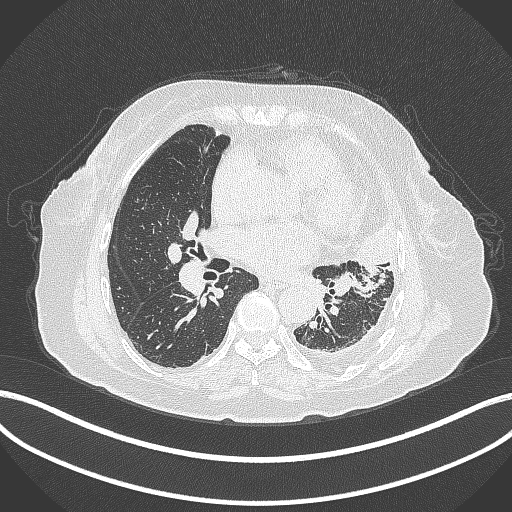
Chest CT, one axial slice. Position 177 of 399 along the scan axis. Reconstruction kernel B70f. 120 kVp. Lung window (W 1500 / L -600 HU). 1 mm slice thickness. 512 × 512 image matrix. Patient: female, 75 years. Case-level facts recorded for this patient, not image findings: clinical TNM (as recorded): T3 N3 M1.
Annotated regions visible in this slice (bounding box drawn by a radiologist):
- lung tumour (recorded histology: adenocarcinoma): bounding box [x1, y1, x2, y2] px = [350, 214, 398, 273]